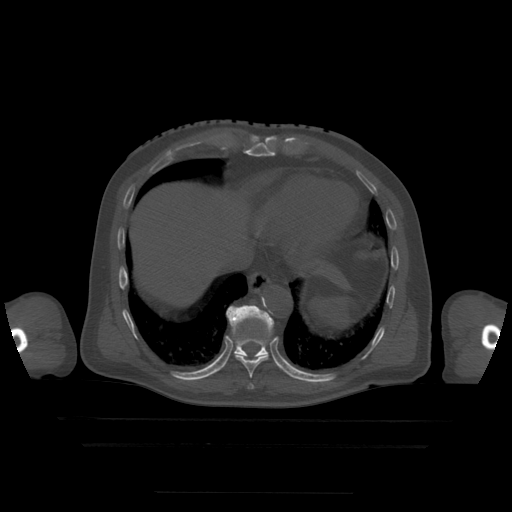
CT including the spine, one axial slice; position 253 of 522 along the scan axis; bone window (W 1800 / L 400 HU); 512 × 512 image matrix. Patient age 68 years. From the clinical record (not read from this slice): primary cancer: urothelial.
Structures marked on this image (semi-automatically segmented with operator editing):
- T10 vertebra: box from (x=226, y=306) to (x=274, y=357) px
- T9 vertebra: (x=230, y=323)–(x=271, y=390)